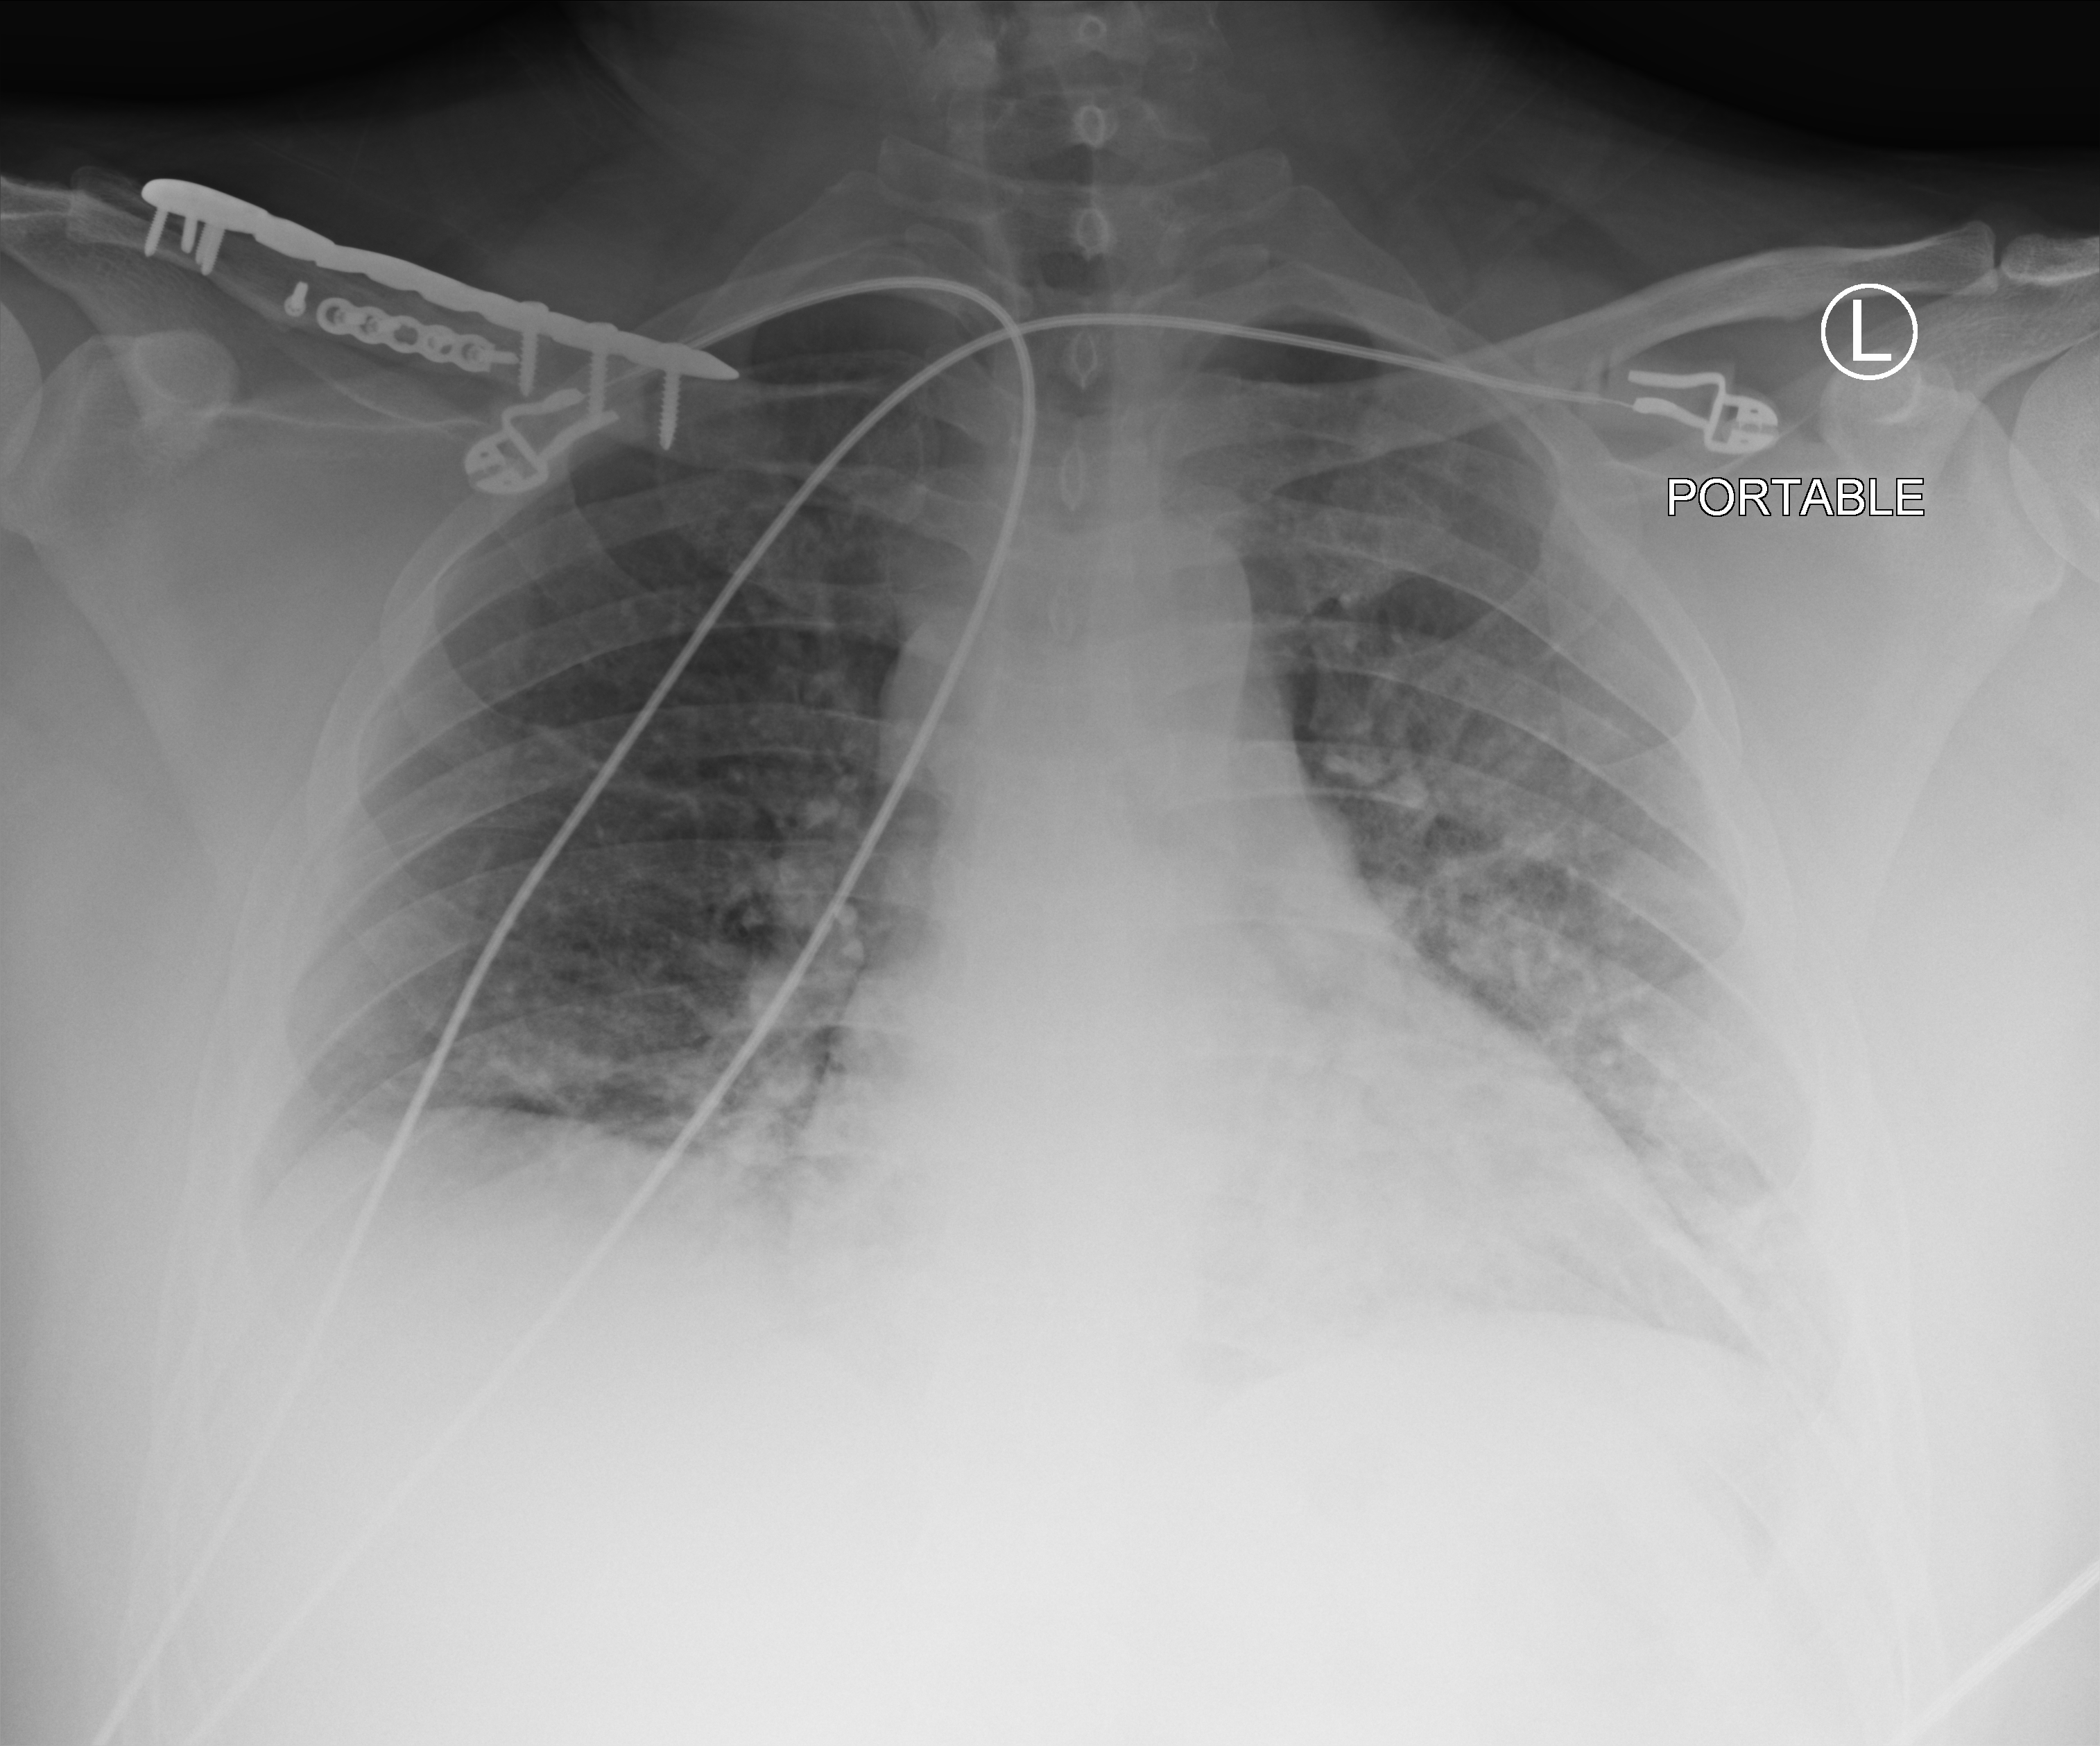
Chest X-ray (portable). Male patient hospitalised with COVID-19, age 18–59 years.
Hospital-stay facts (about this admission, not read from this image; timing relative to this image not recorded): admitted to intensive care during this hospital stay: no; mechanically ventilated during this hospital stay: no.